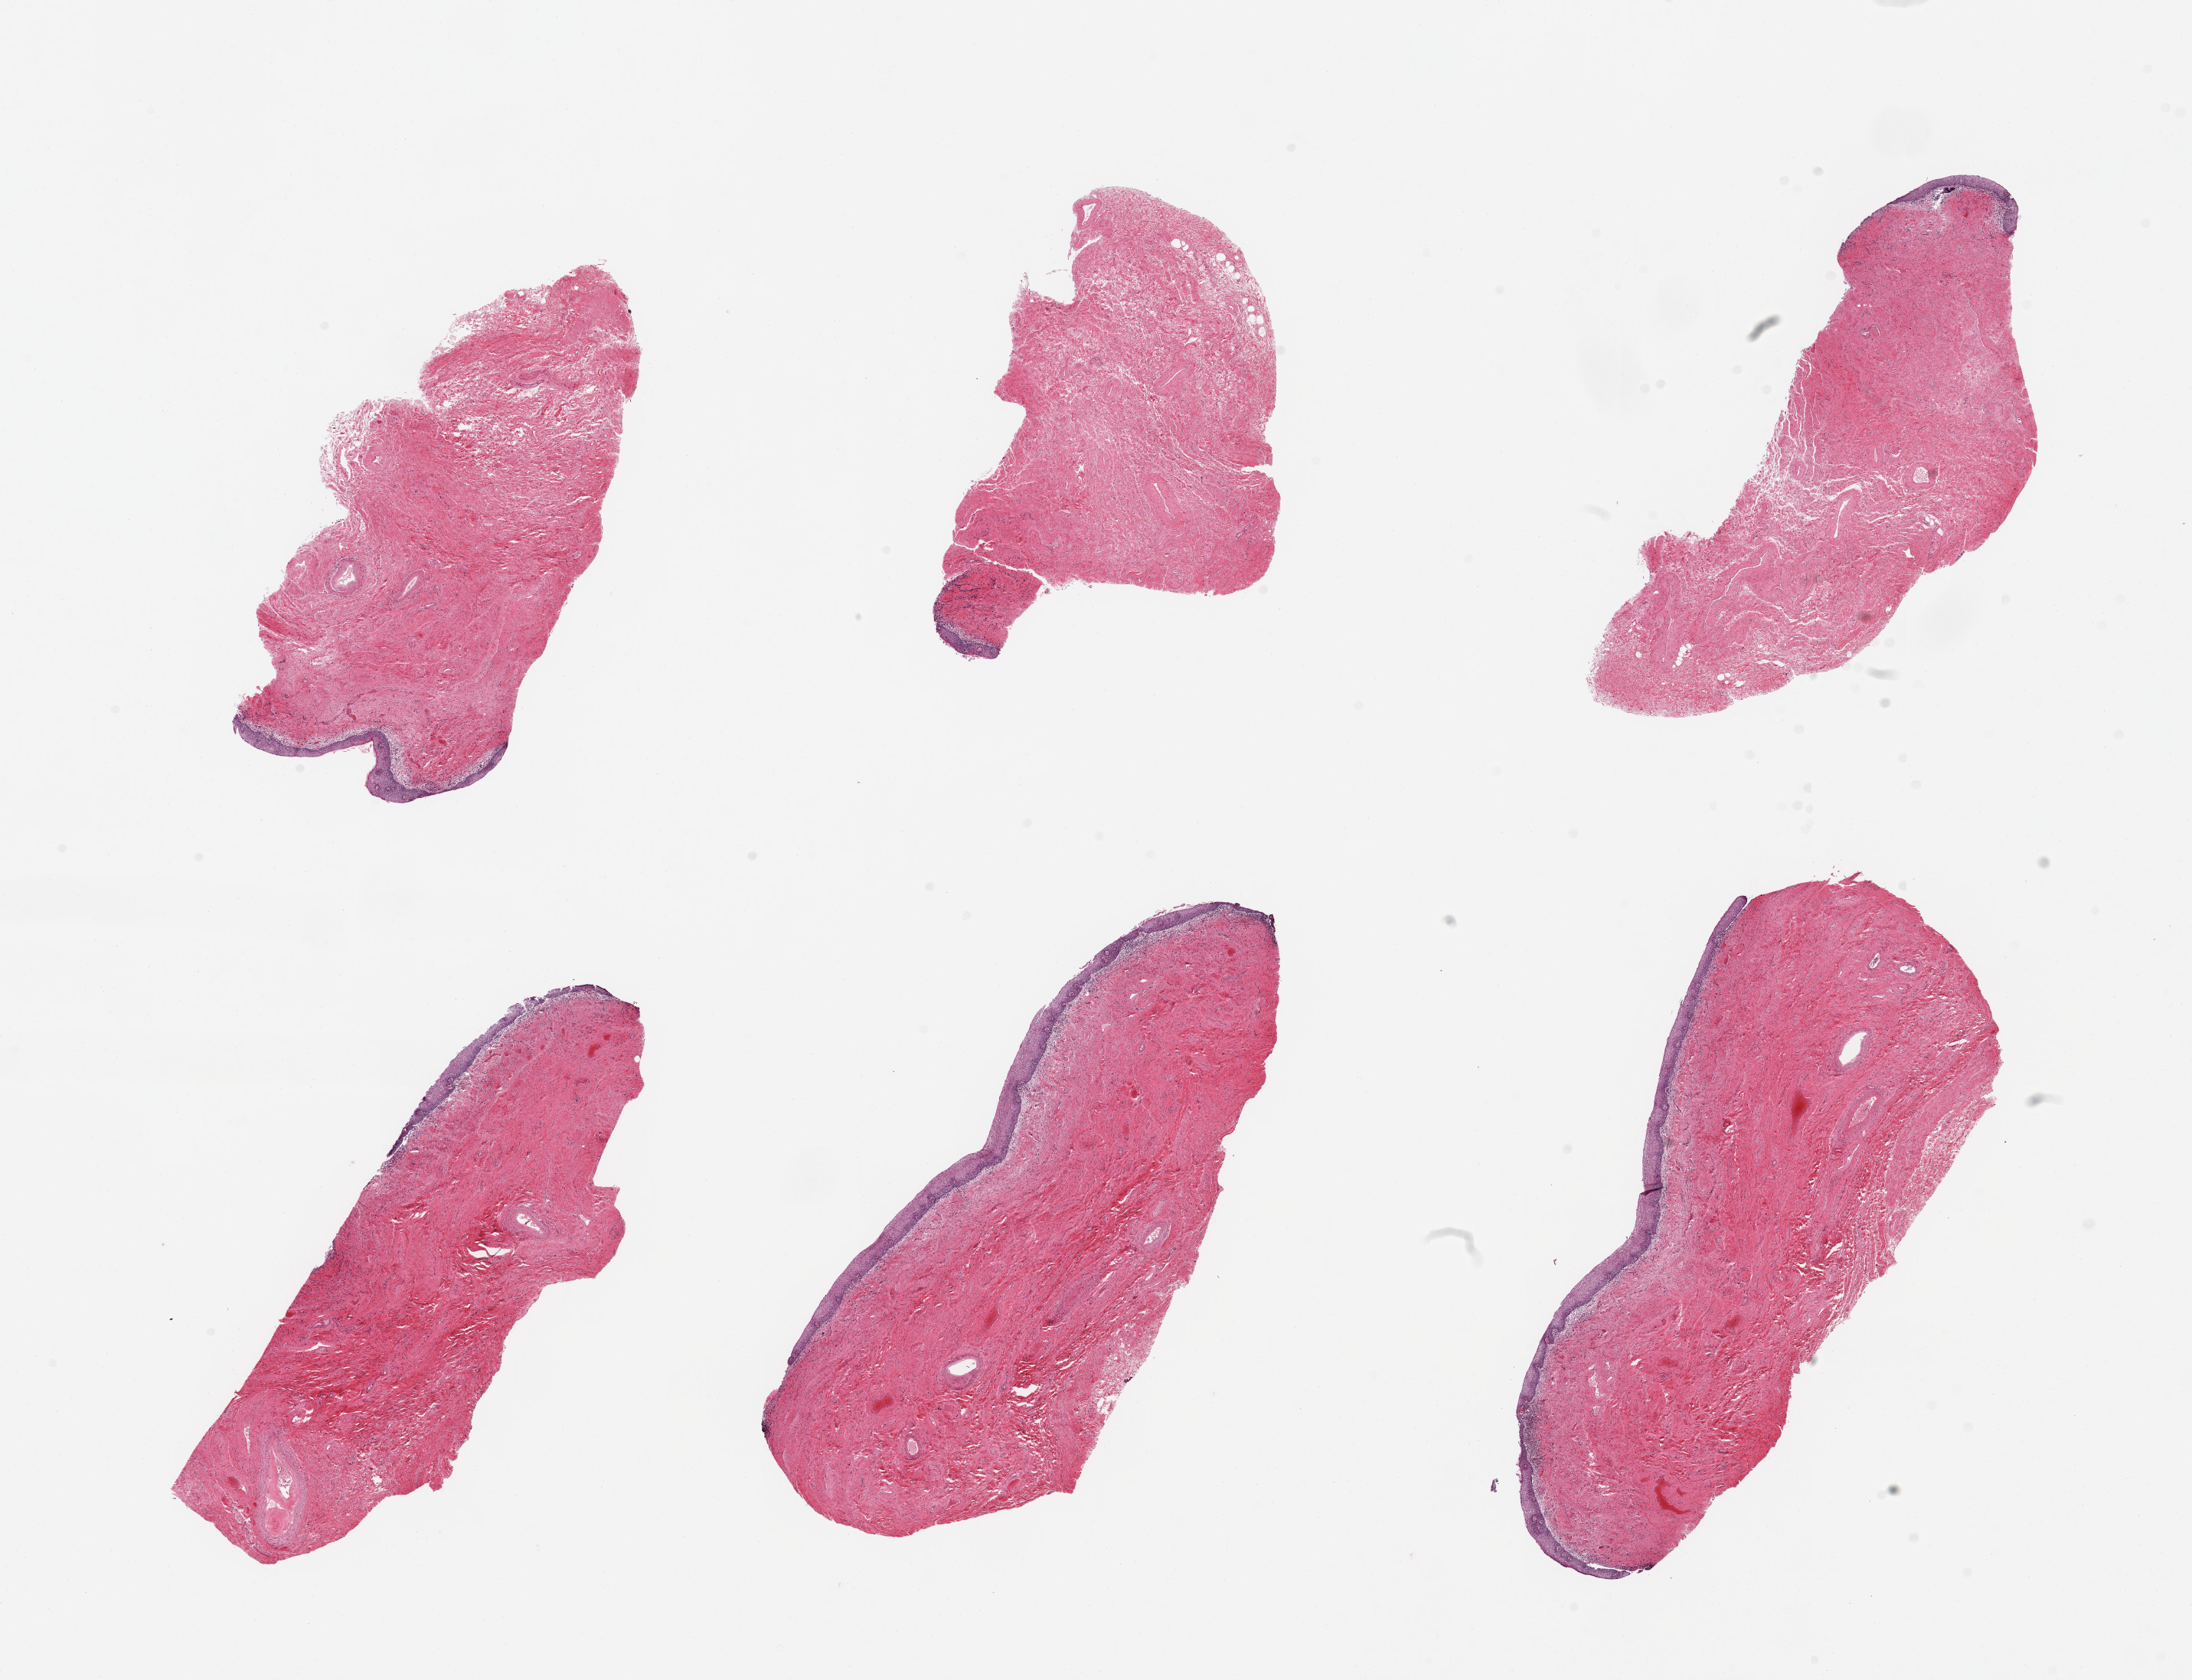
Digitized hematoxylin and eosin (H&E)-stained section, brightfield, shown as a low-resolution overview of the whole scanned area (about 22.6 x 17.4 mm, slide scanned at 20x), PAXgene-fixed, paraffin-embedded tissue, target tissue: vagina, tissue donor sample. Donor sex: female.
Pathologist's review note for this sample: 6 pieces; diffuse lympho-plasmacytic infiltrate beneath squamous epithelium, congested, thick-walled stromal vessels; squamous epithelium ~0.2mm.